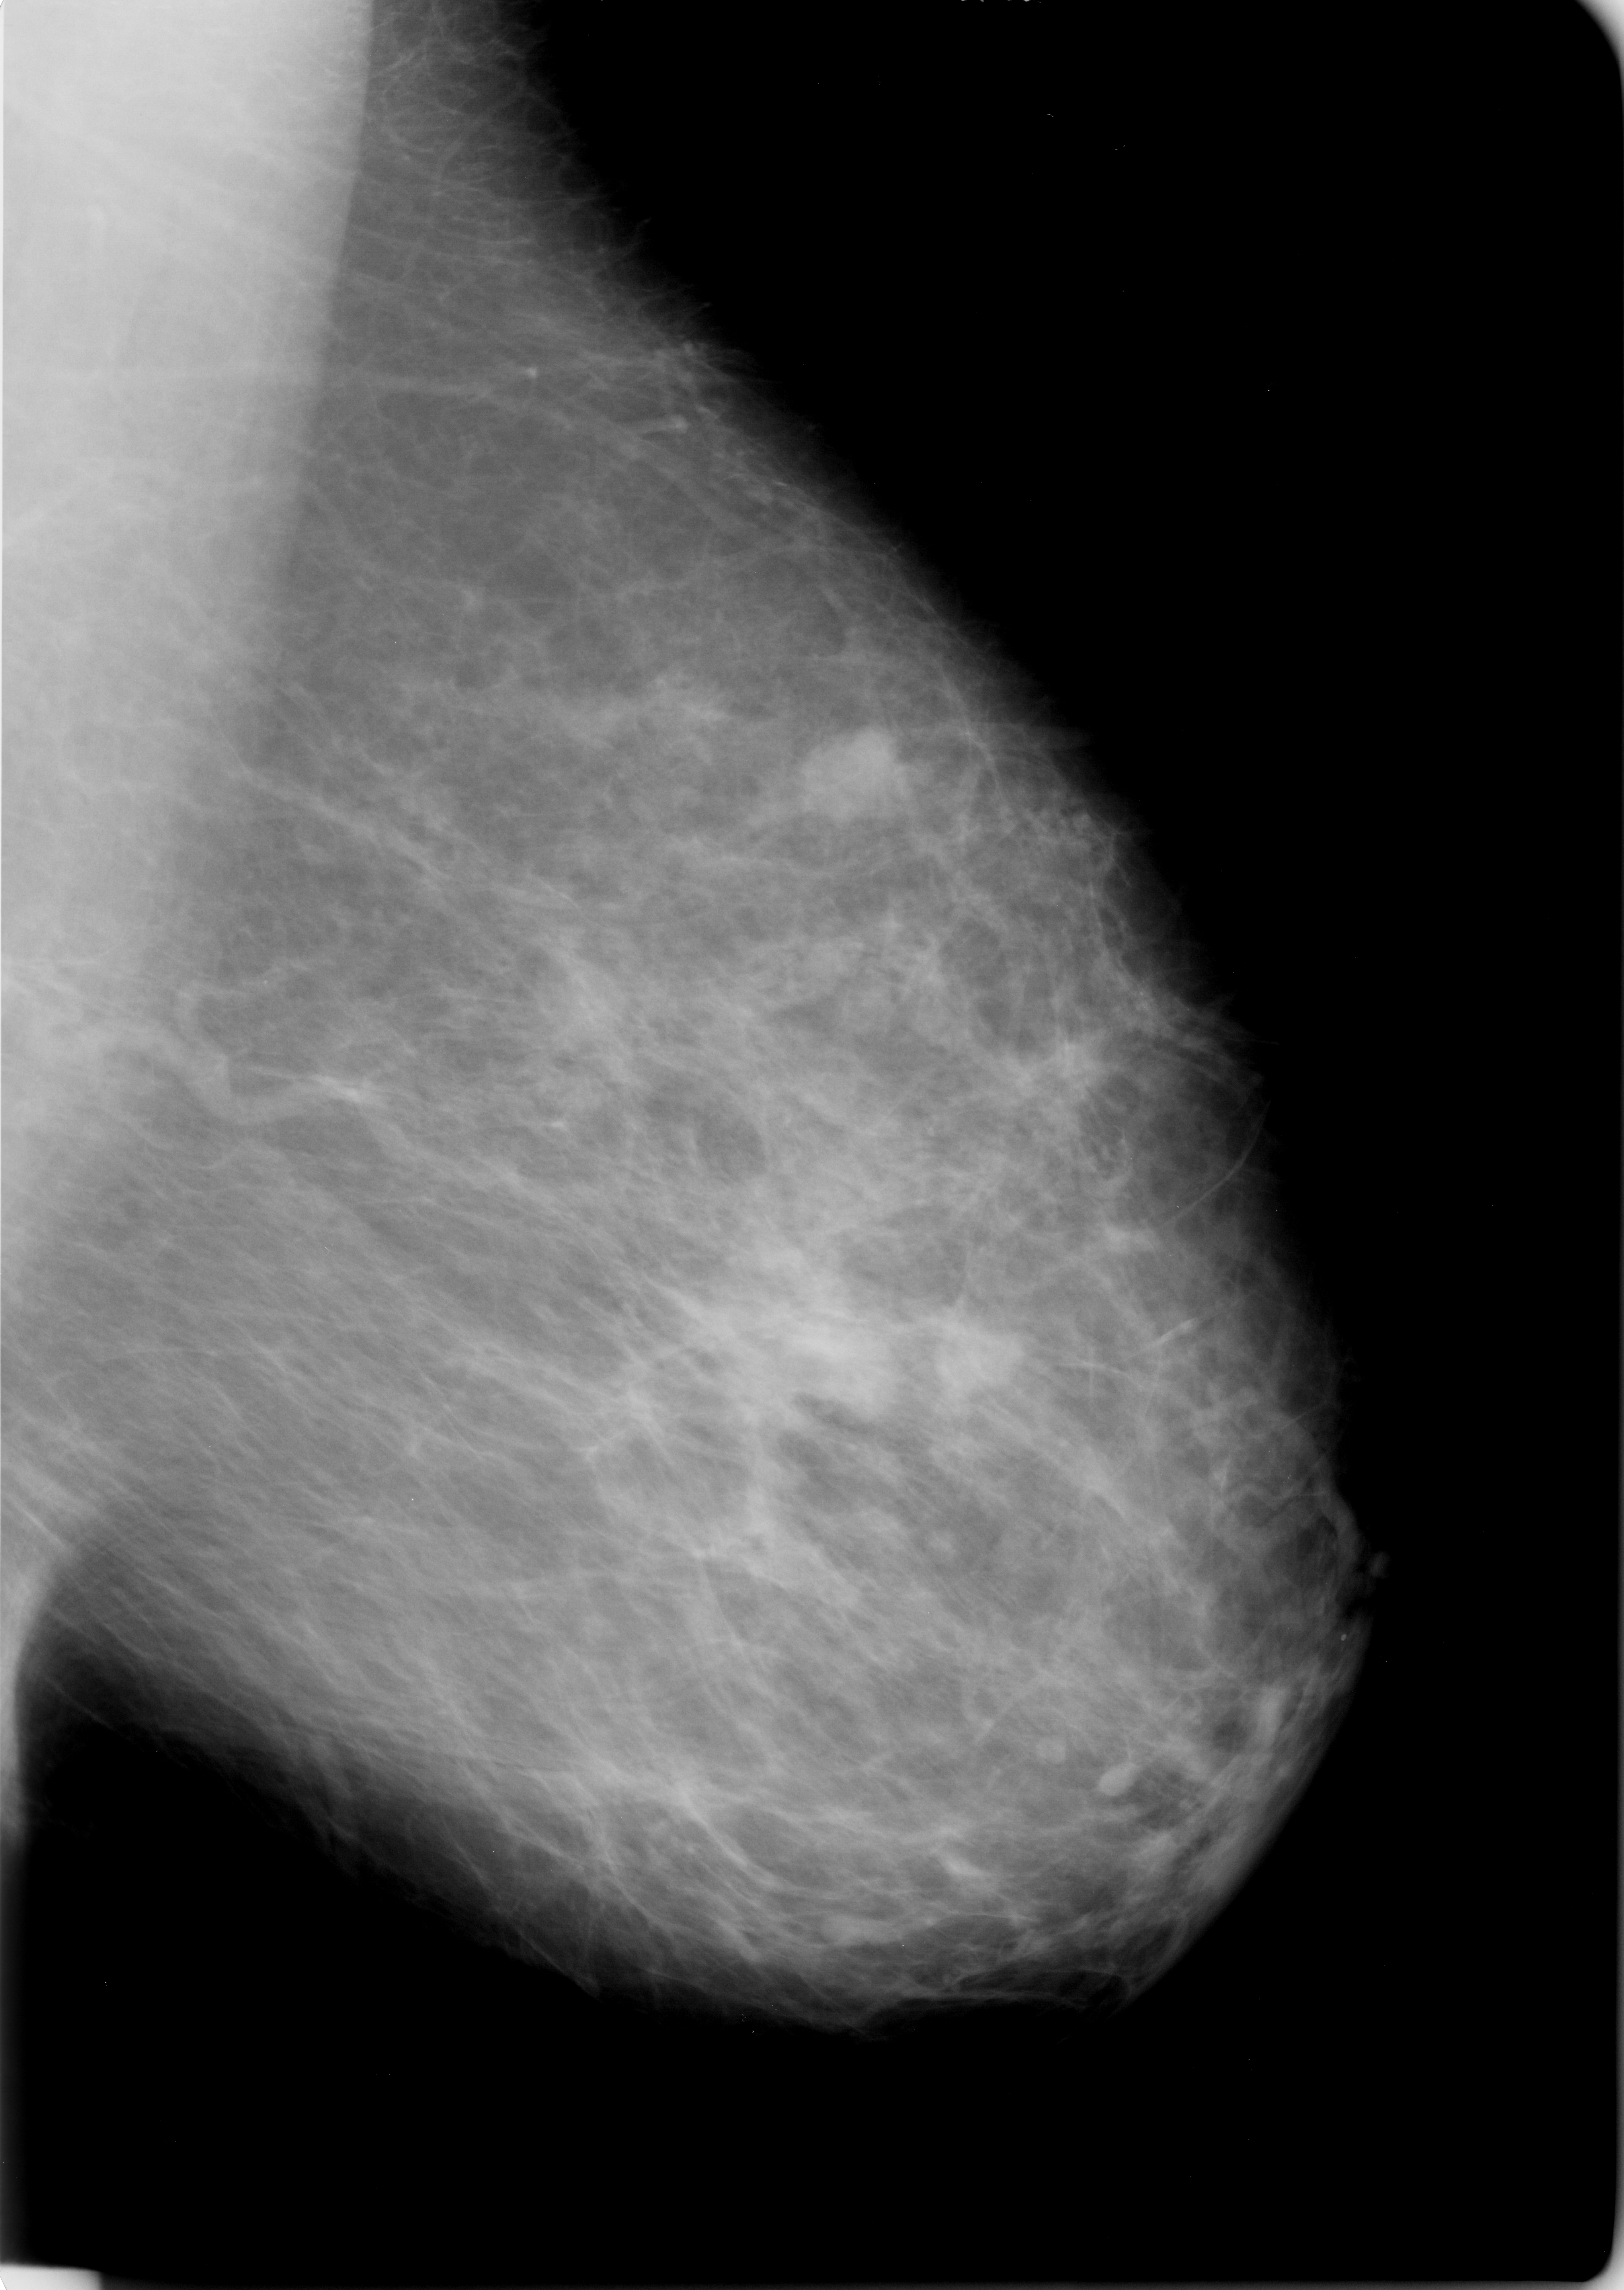
Digitized screen-film mammogram, left breast, MLO view, BI-RADS breast density category 3 (scale 1–4).
- Abnormality record for this image: Finding 1 of 3: mass, shape lobulated, margins circumscribed / ill defined; BI-RADS assessment category 3; subtlety rating 3 on a 1 (subtle) to 5 (obvious) scale; pathology result (as recorded, not read from the image): malignant.
- Finding 2 of 3: mass, shape lobulated, margins circumscribed / ill defined; BI-RADS assessment category 3; pathology result (as recorded, not read from the image): malignant.
- Finding 3 of 3: mass, shape lobulated, margins circumscribed / ill defined; BI-RADS assessment category 3; subtlety rating 3 on a 1 (subtle) to 5 (obvious) scale; pathology (as recorded): malignant.